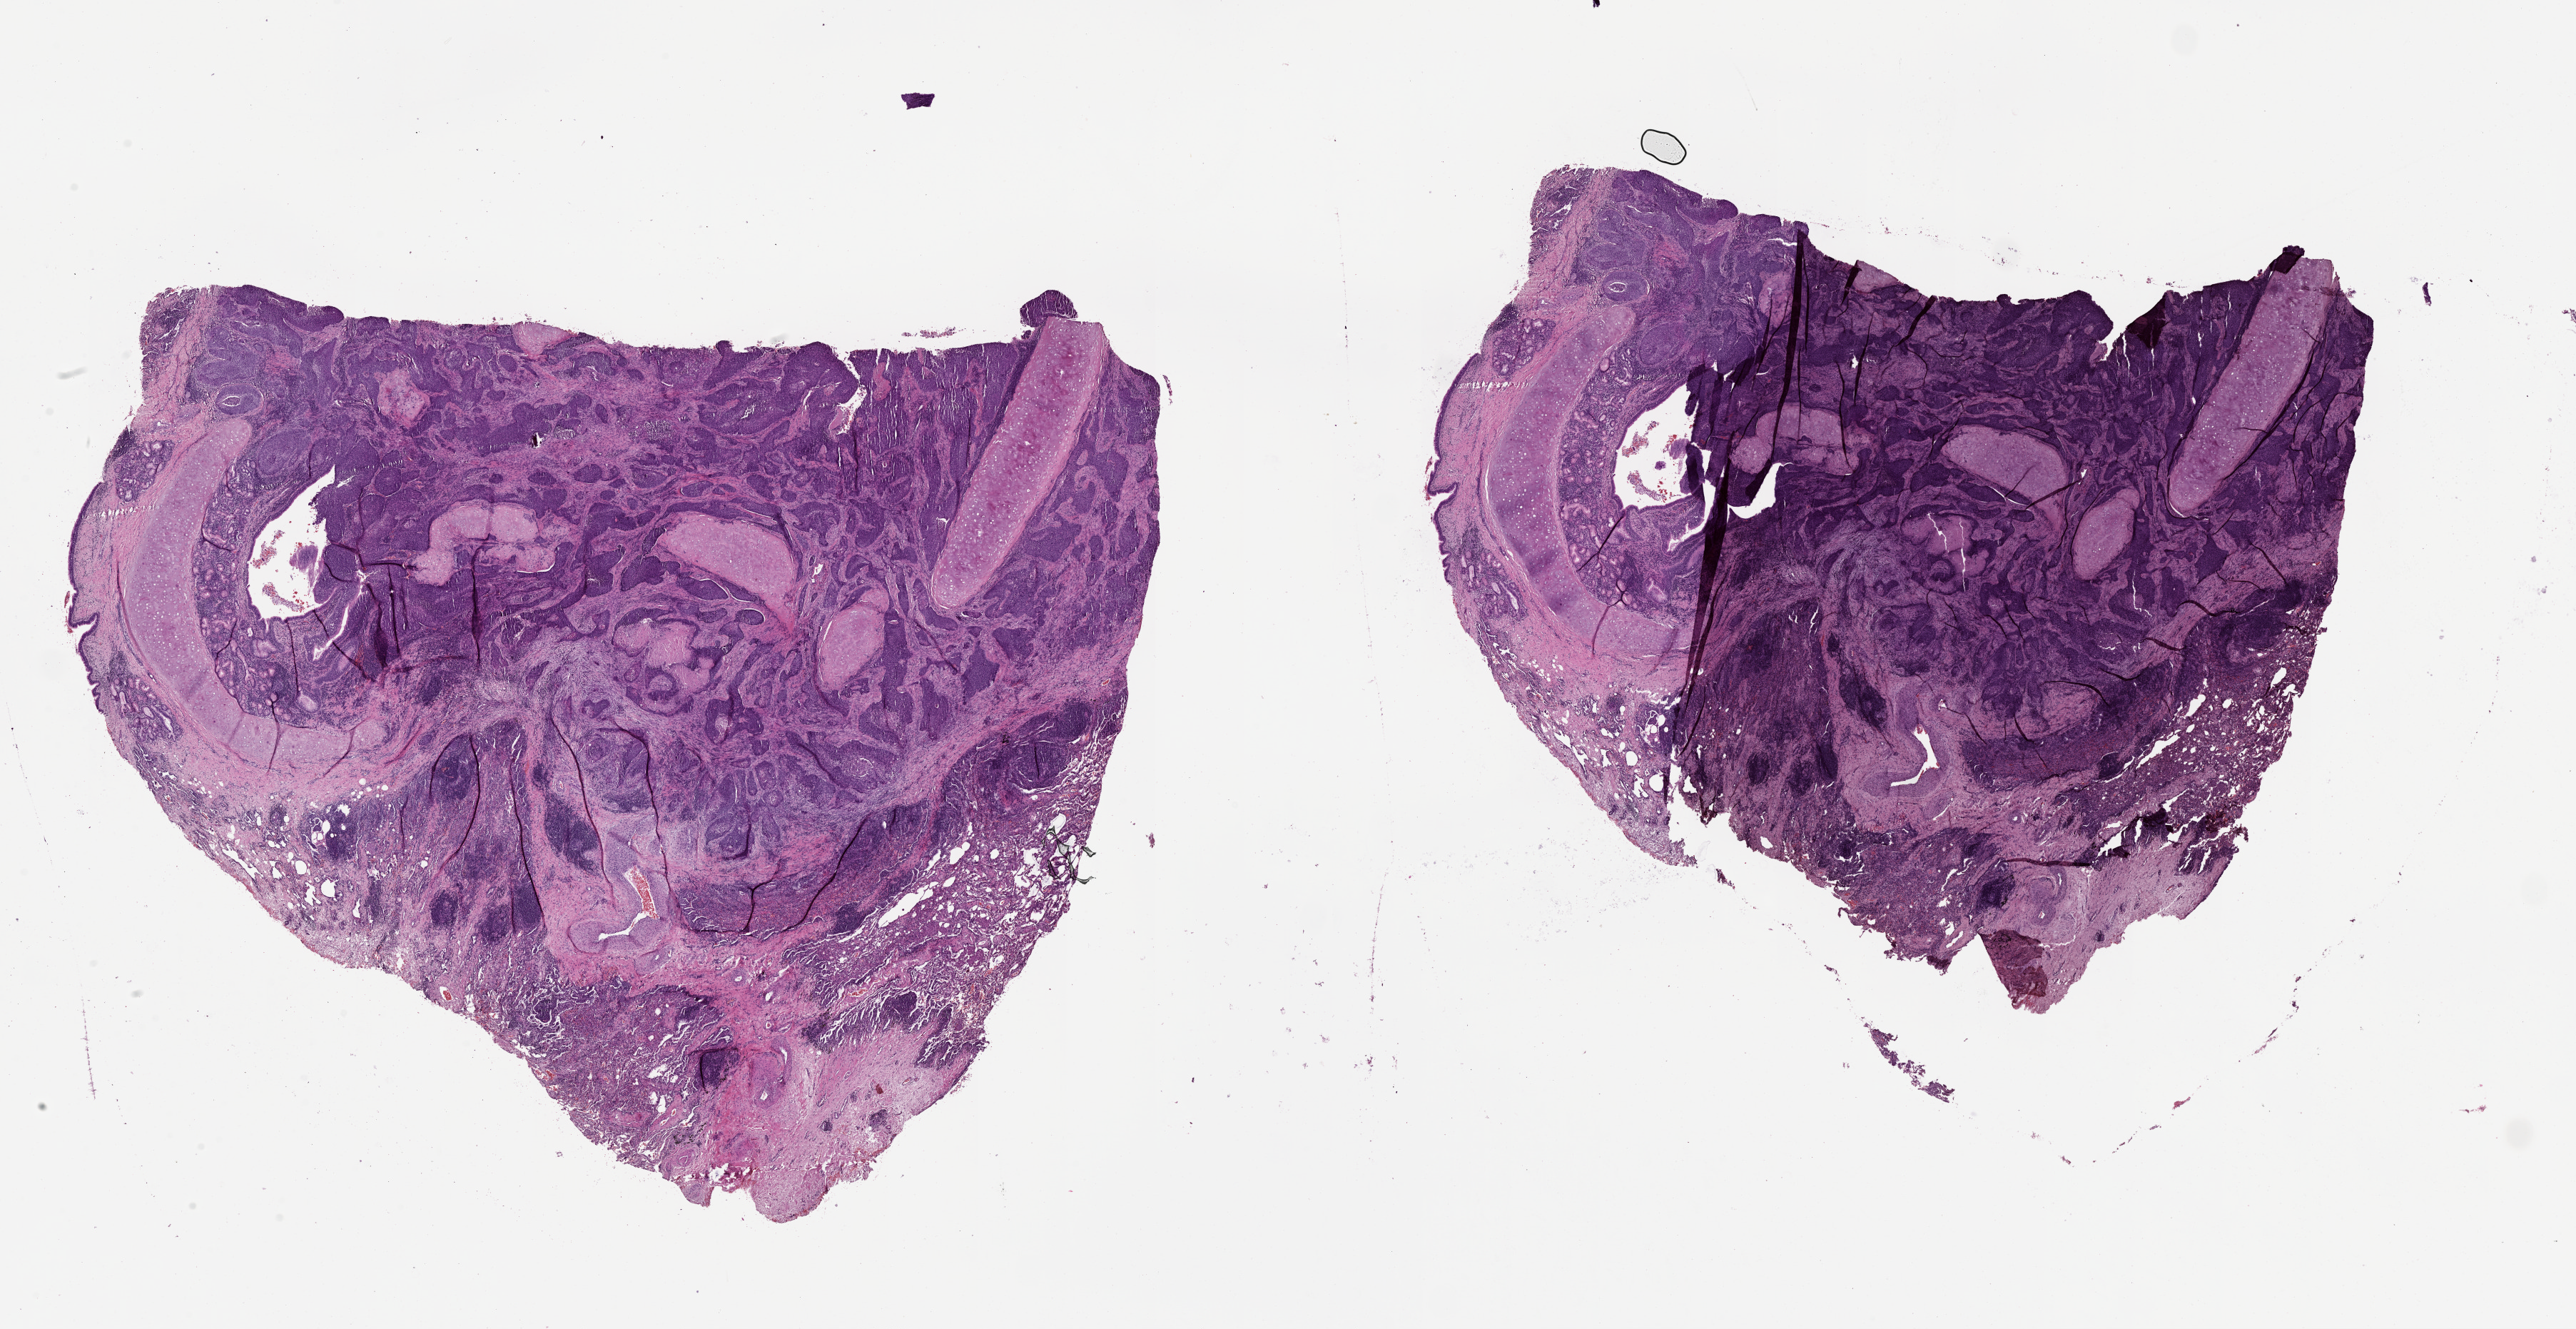
Whole-slide histology image, H&E, low-resolution overview of the scanned area, about 29.1 x 15.0 mm (acquisition: 20x scan), tumour tissue sample, lung. 53-year-old male patient.
Patient diagnosis (cohort enrolment): squamous cell carcinoma (lung).